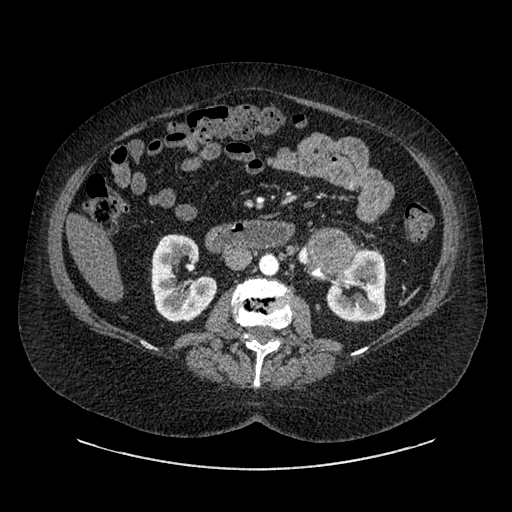
Contrast-enhanced abdominal CT, one axial slice. Position 493 of 769 along the scan axis. Reconstruction kernel SOFT. Soft-tissue window (W 400 / L 40 HU). 512 × 512 image matrix, field of view 460 × 460 mm. Female patient, age 61 years. From the clinical record (not read from this slice): diagnosis: adrenocortical carcinoma; tumour side: left adrenal; tumour size at pathology: 13 cm; Ki-67 index: 79 %; stage (as recorded): 2.
Outlined on this slice (semi-automatically segmented with operator editing):
- mass: bounding box [x1, y1, x2, y2] px = [314, 233, 352, 272]